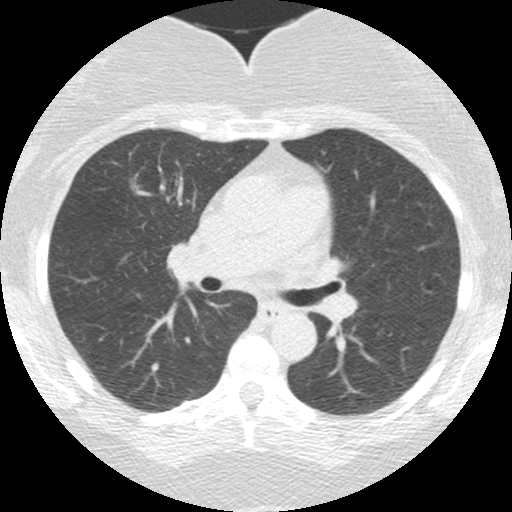
Low-dose screening chest CT, one axial slice; slice 97 of 150 in the series (ordered by position); 120 kVp; lung window (W 1500 / L -600 HU); 2.5 mm slice thickness; 512 × 512 image matrix, field of view 286 × 286 mm.
Structures marked on this image (manually delineated by an expert):
- lesion 1 (tumor, upper lobe of right lung): bounding box [x1, y1, x2, y2] px = [130, 178, 140, 193]